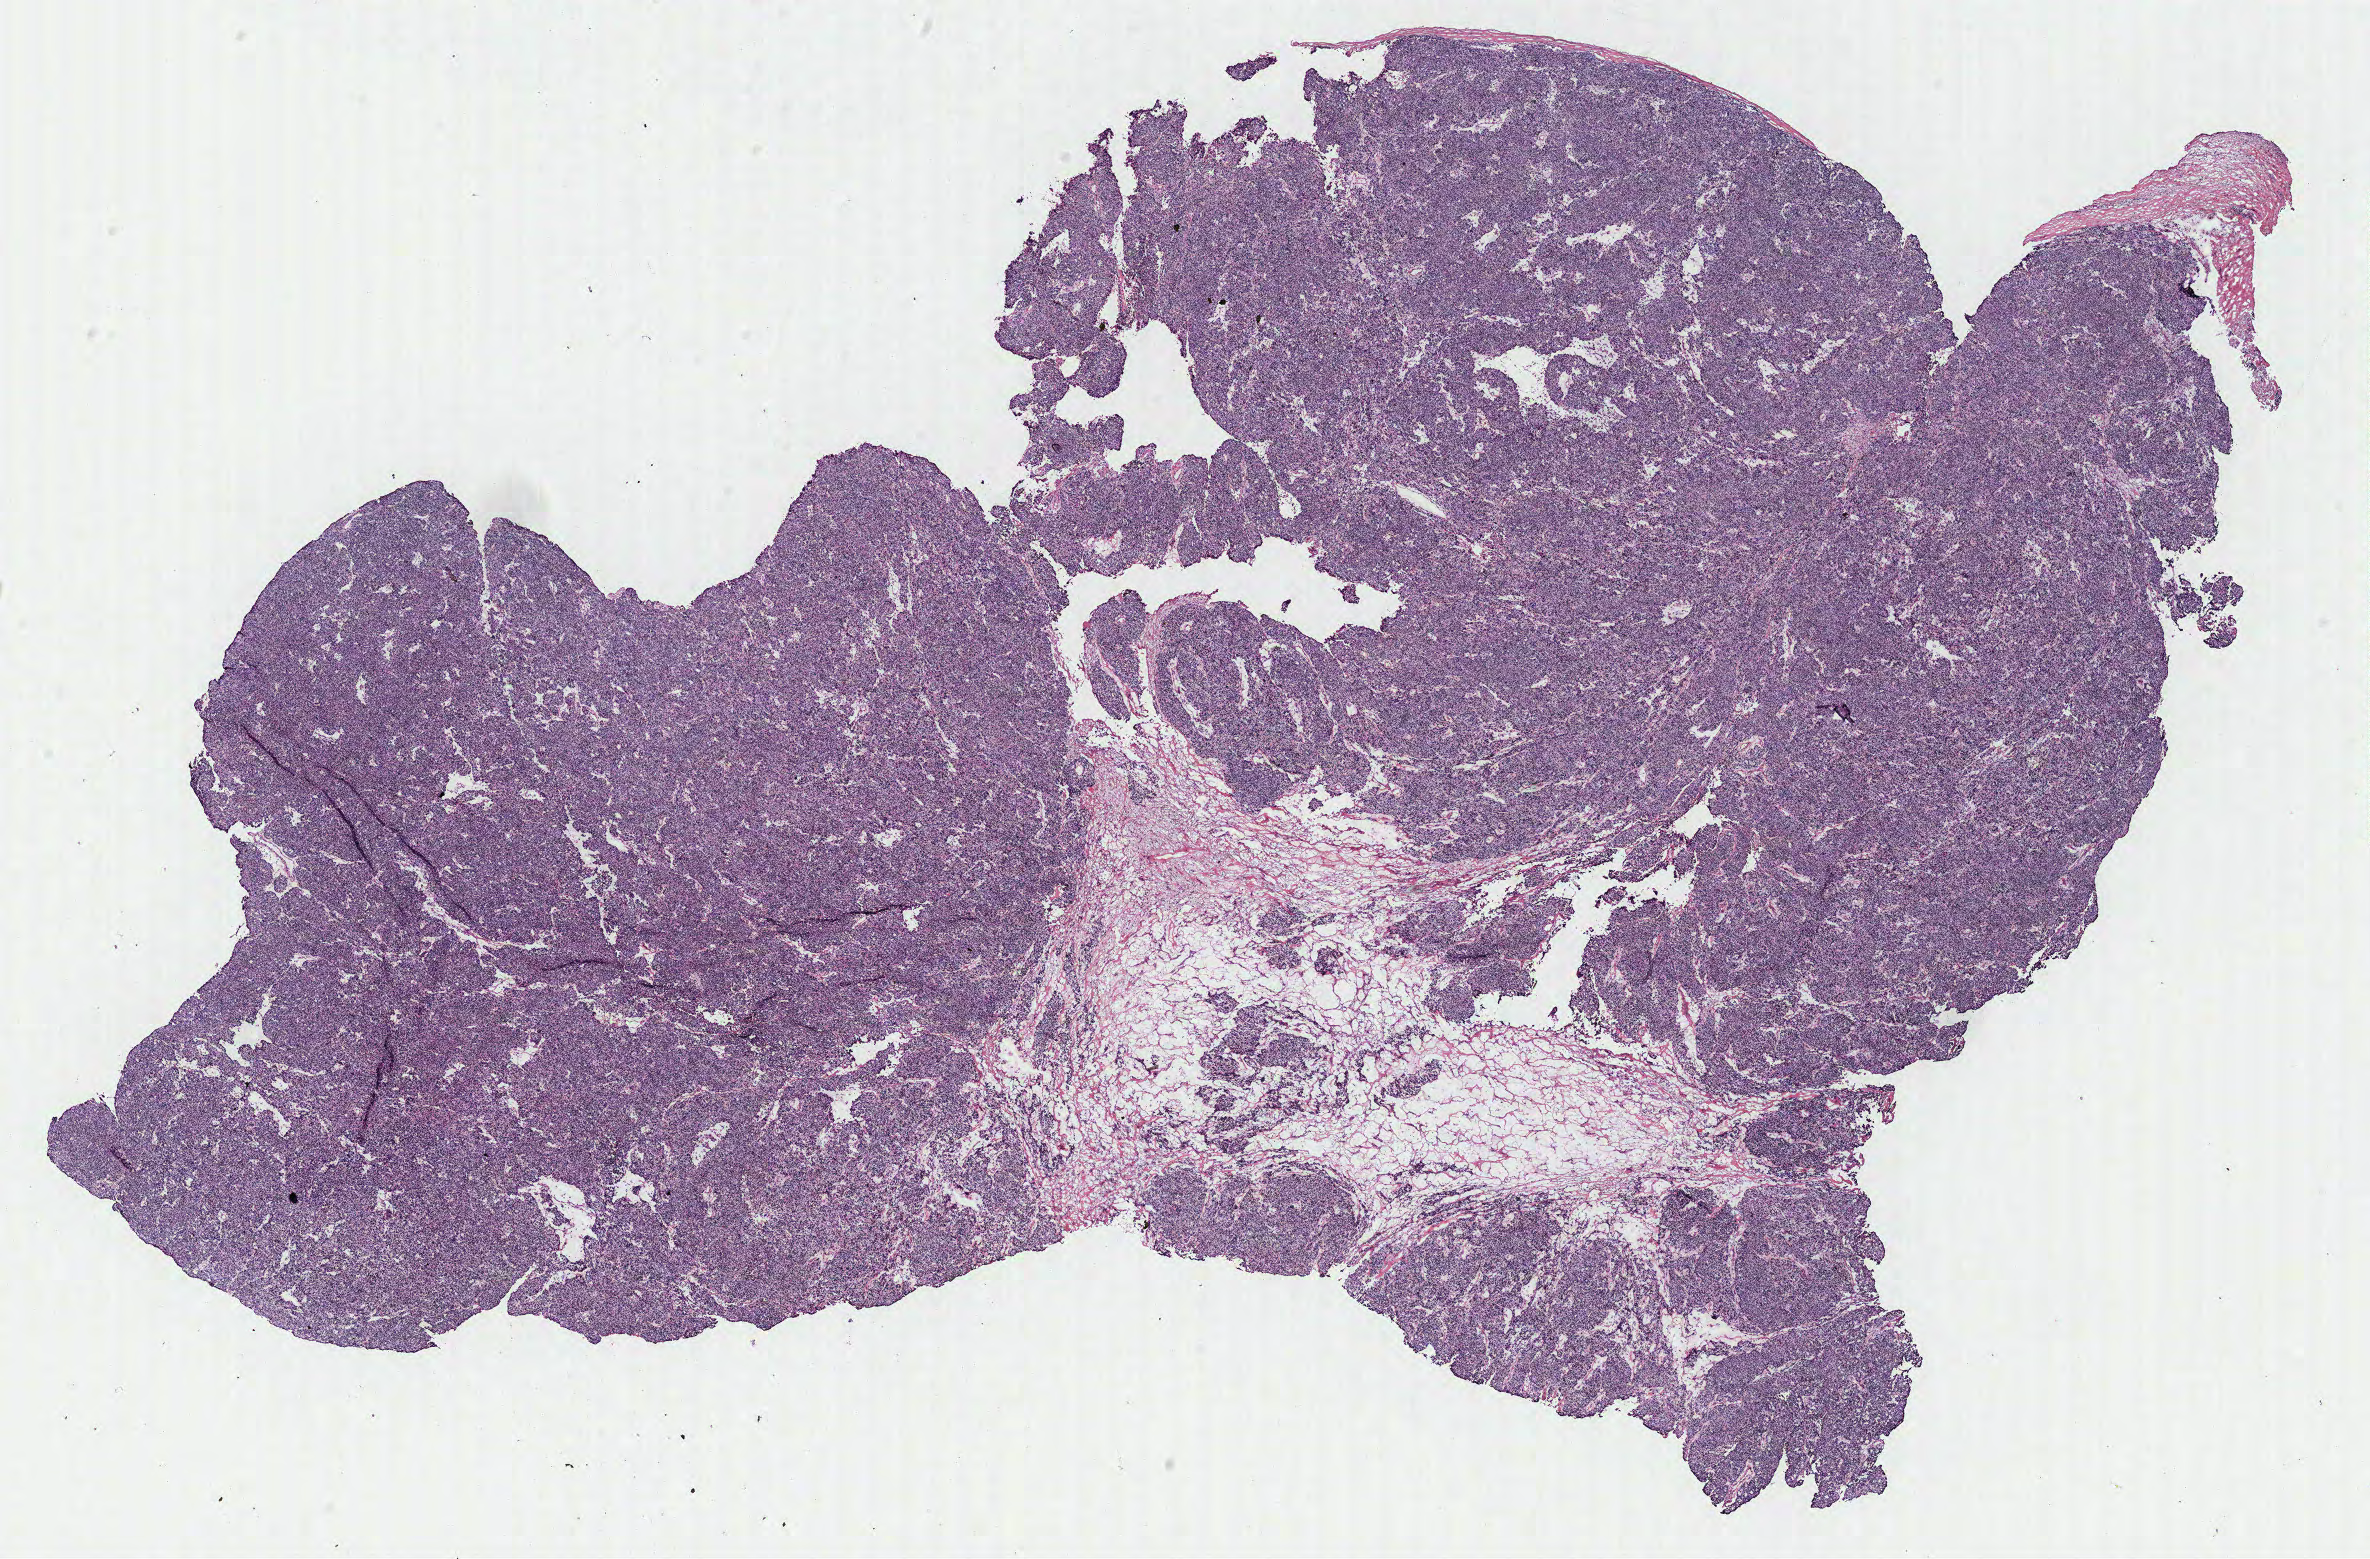
Digitized H&E tissue section (whole slide), whole scanned area (about 19.0 x 12.5 mm, slide scanned at 40x) shown as a low-resolution overview, tumour tissue sample, ovary. 51-year-old female patient.
Diagnosis: Serous adenocarcinoma, NOS. Primary tumour site (as recorded): ovary.